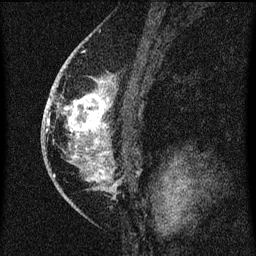
Breast MRI (dynamic contrast-enhanced), one sagittal slice. Position 42 of 60 along the scan axis. Dynamic contrast-enhanced series, image 2 of 3 at this slice position (ordered by acquisition). 1.5 T. TE 4.2 ms, TR 8 ms. 256 × 256 image matrix, field of view 180 × 180 mm. Patient: female, 46 years.
Structures marked on this image (semi-automatically segmented with operator editing):
- analysis volume of interest (the breast-tissue region the enhancement analysis was run in; not a lesion): bounding box [x1, y1, x2, y2] px = [53, 68, 115, 195]
- tumour enhancement mask (voxels above the 70 % enhancement threshold inside the analysis volume of interest): [54, 70, 115, 187]